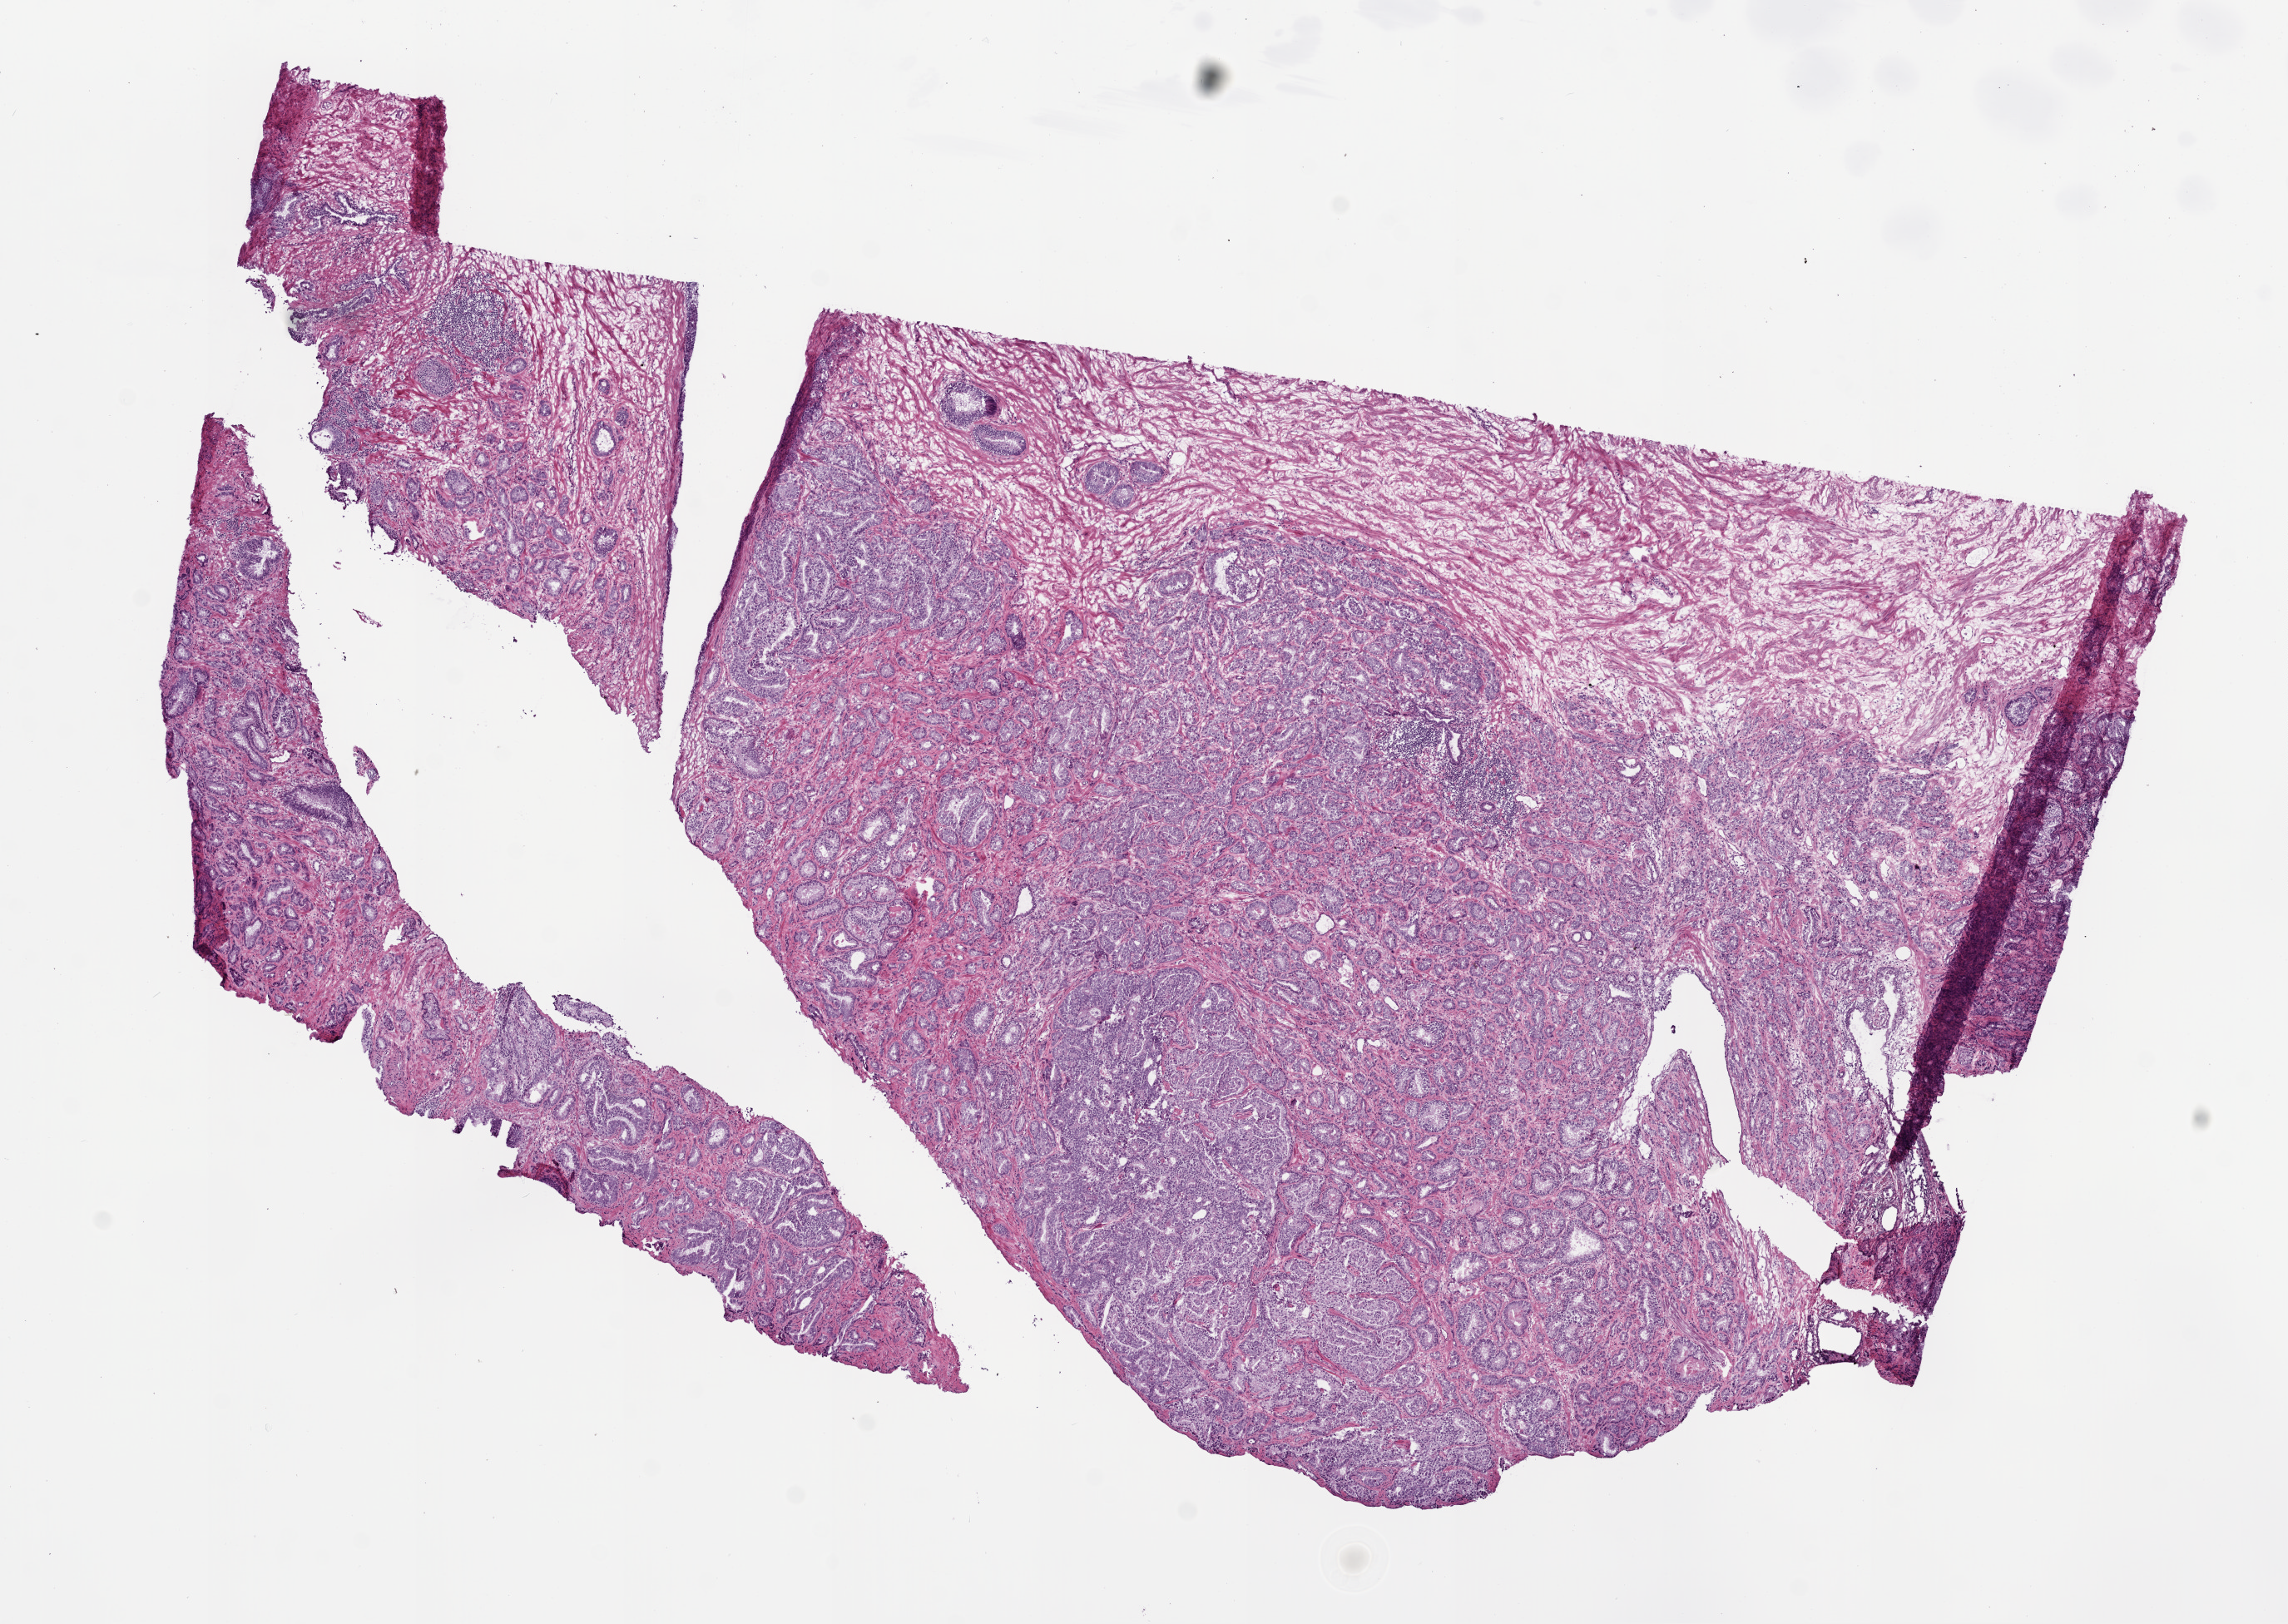
Digitized Hematoxylin and eosin (H&E) stained tissue section (whole slide) — whole scanned area (about 11.0 x 7.8 mm, from a 20x scan) shown as a low-resolution overview; frozen section from the bottom of the tissue portion; prostate, primary tumour sample. Male, age 60 years at initial diagnosis. Gleason score: 7 (3+4). Pathologist review of this section (percent, as recorded): tumour cells 65%, tumour nuclei 65%, normal cells 15%, stromal cells 20%, necrosis 0%. Inflammatory infiltration, as recorded: lymphocyte infiltration 2%, monocyte infiltration 0%, neutrophil infiltration 0%.
* pathologic diagnosis: Acinar cell carcinoma
* lymph nodes positive (case pathology): 0 of 20 examined
* laterality: right